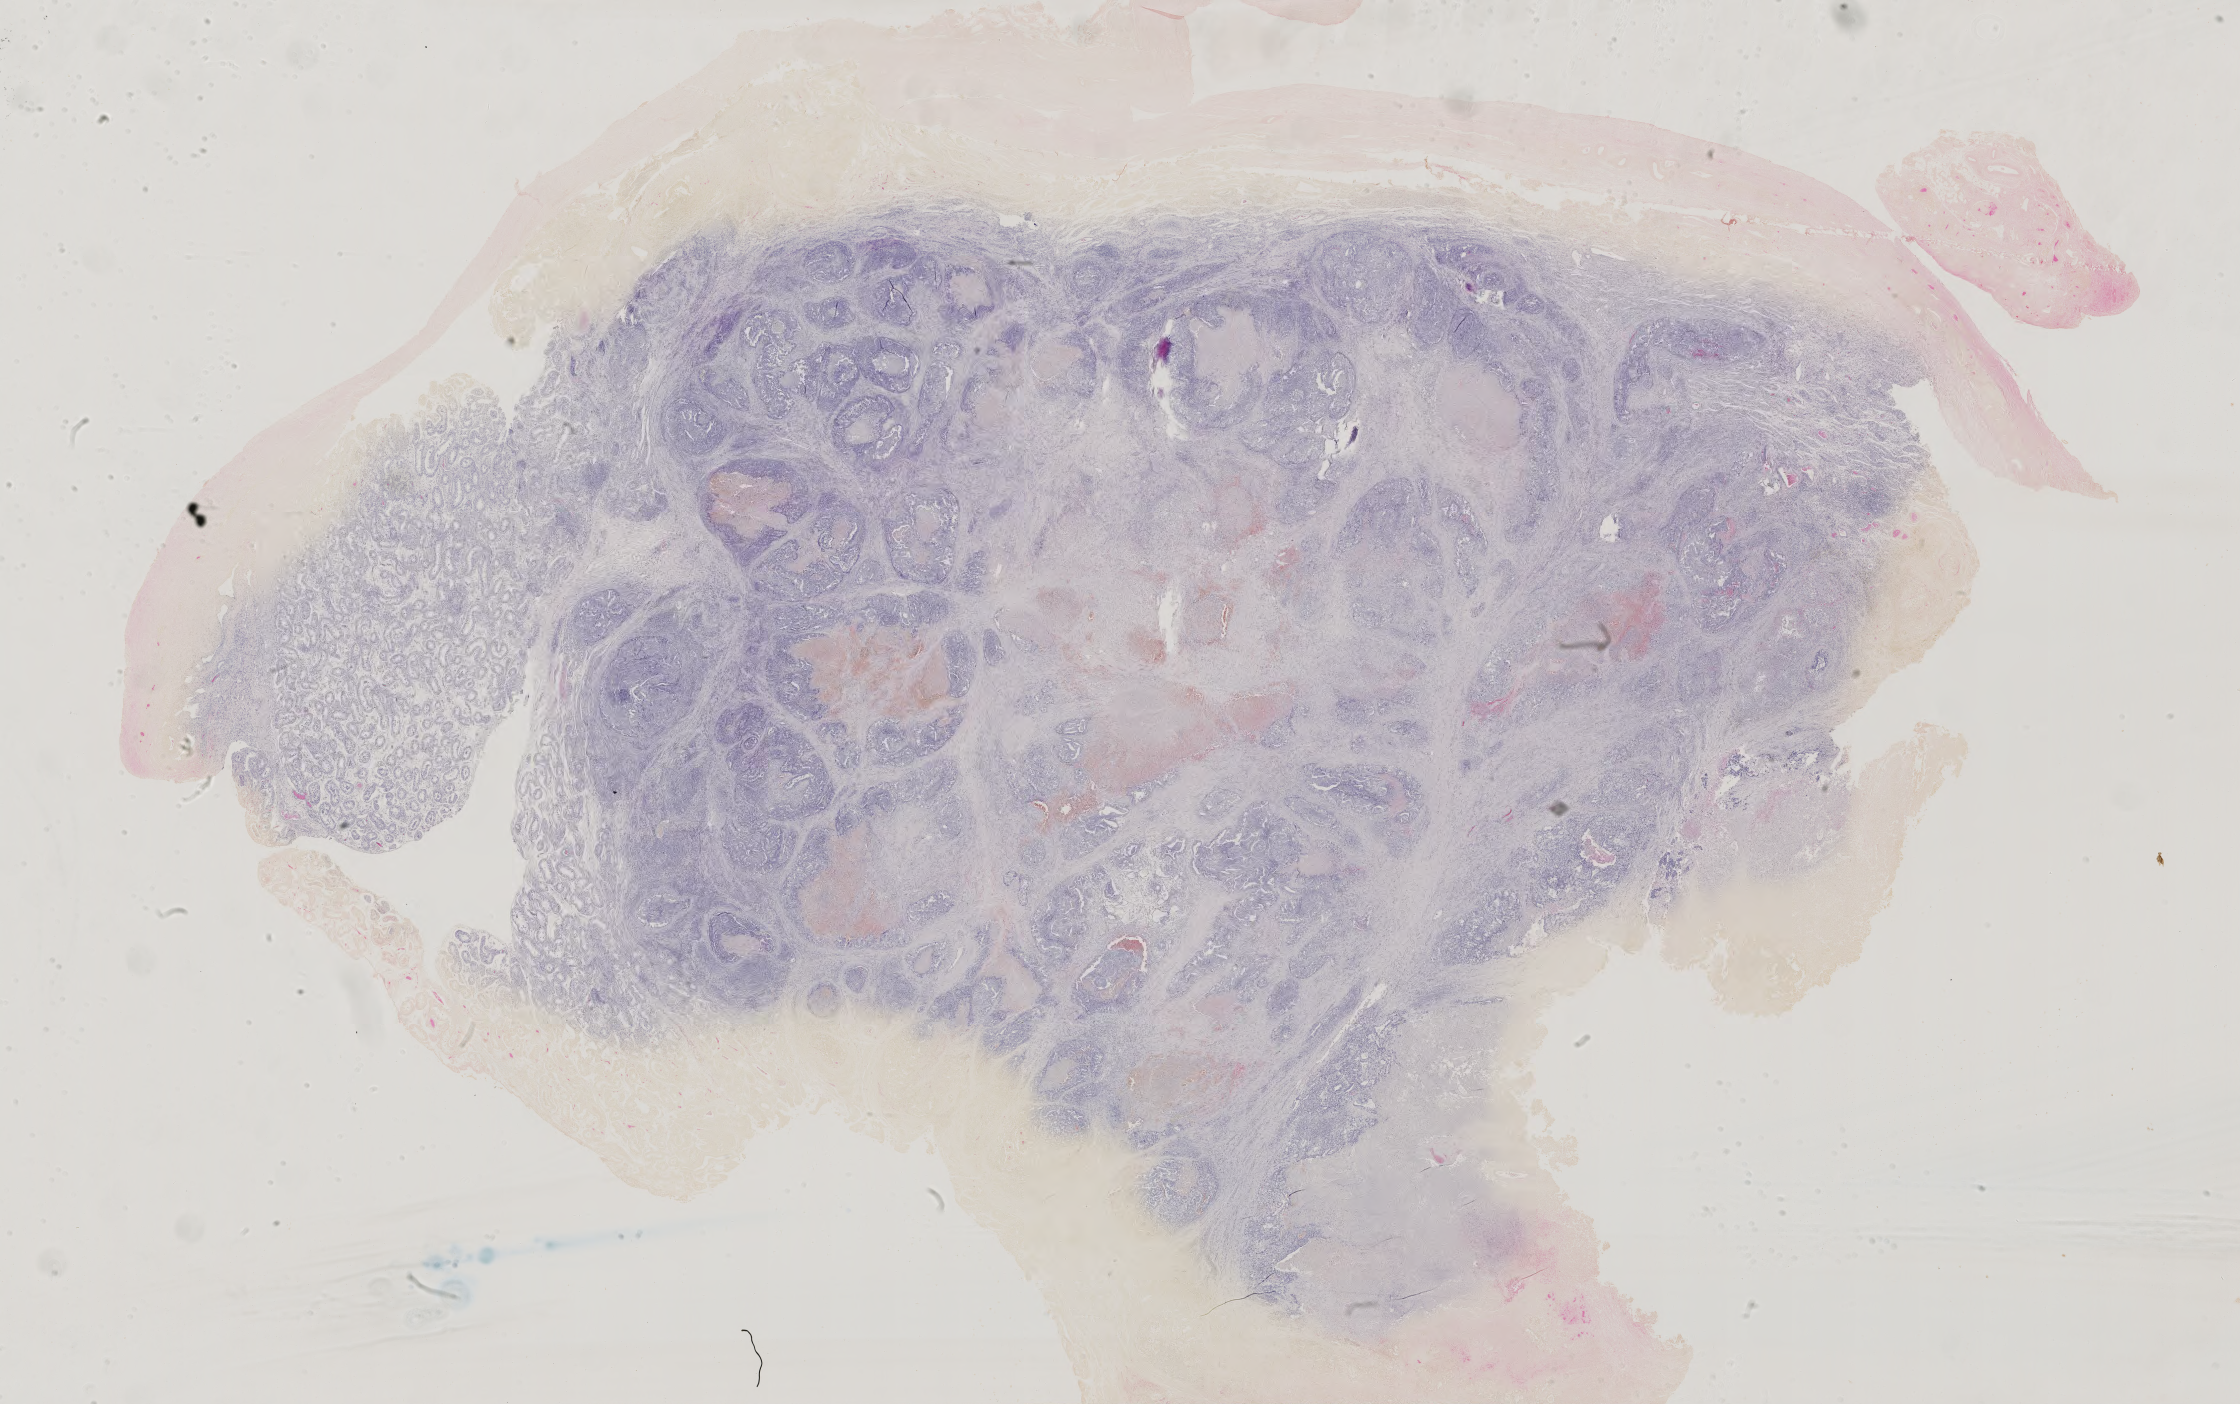
Whole-slide histology image, H&E, a low-resolution overview of the entire scanned area, about 32.6 x 20.5 mm (slide scanned at 40x), FFPE section, testis, primary tumour sample. Patient: male, age at initial diagnosis 18 years.
- diagnosis: Embryonal carcinoma, NOS
- laterality: right
- TNM: T2 NX M0
- AJCC pathologic stage: III (4th edition)